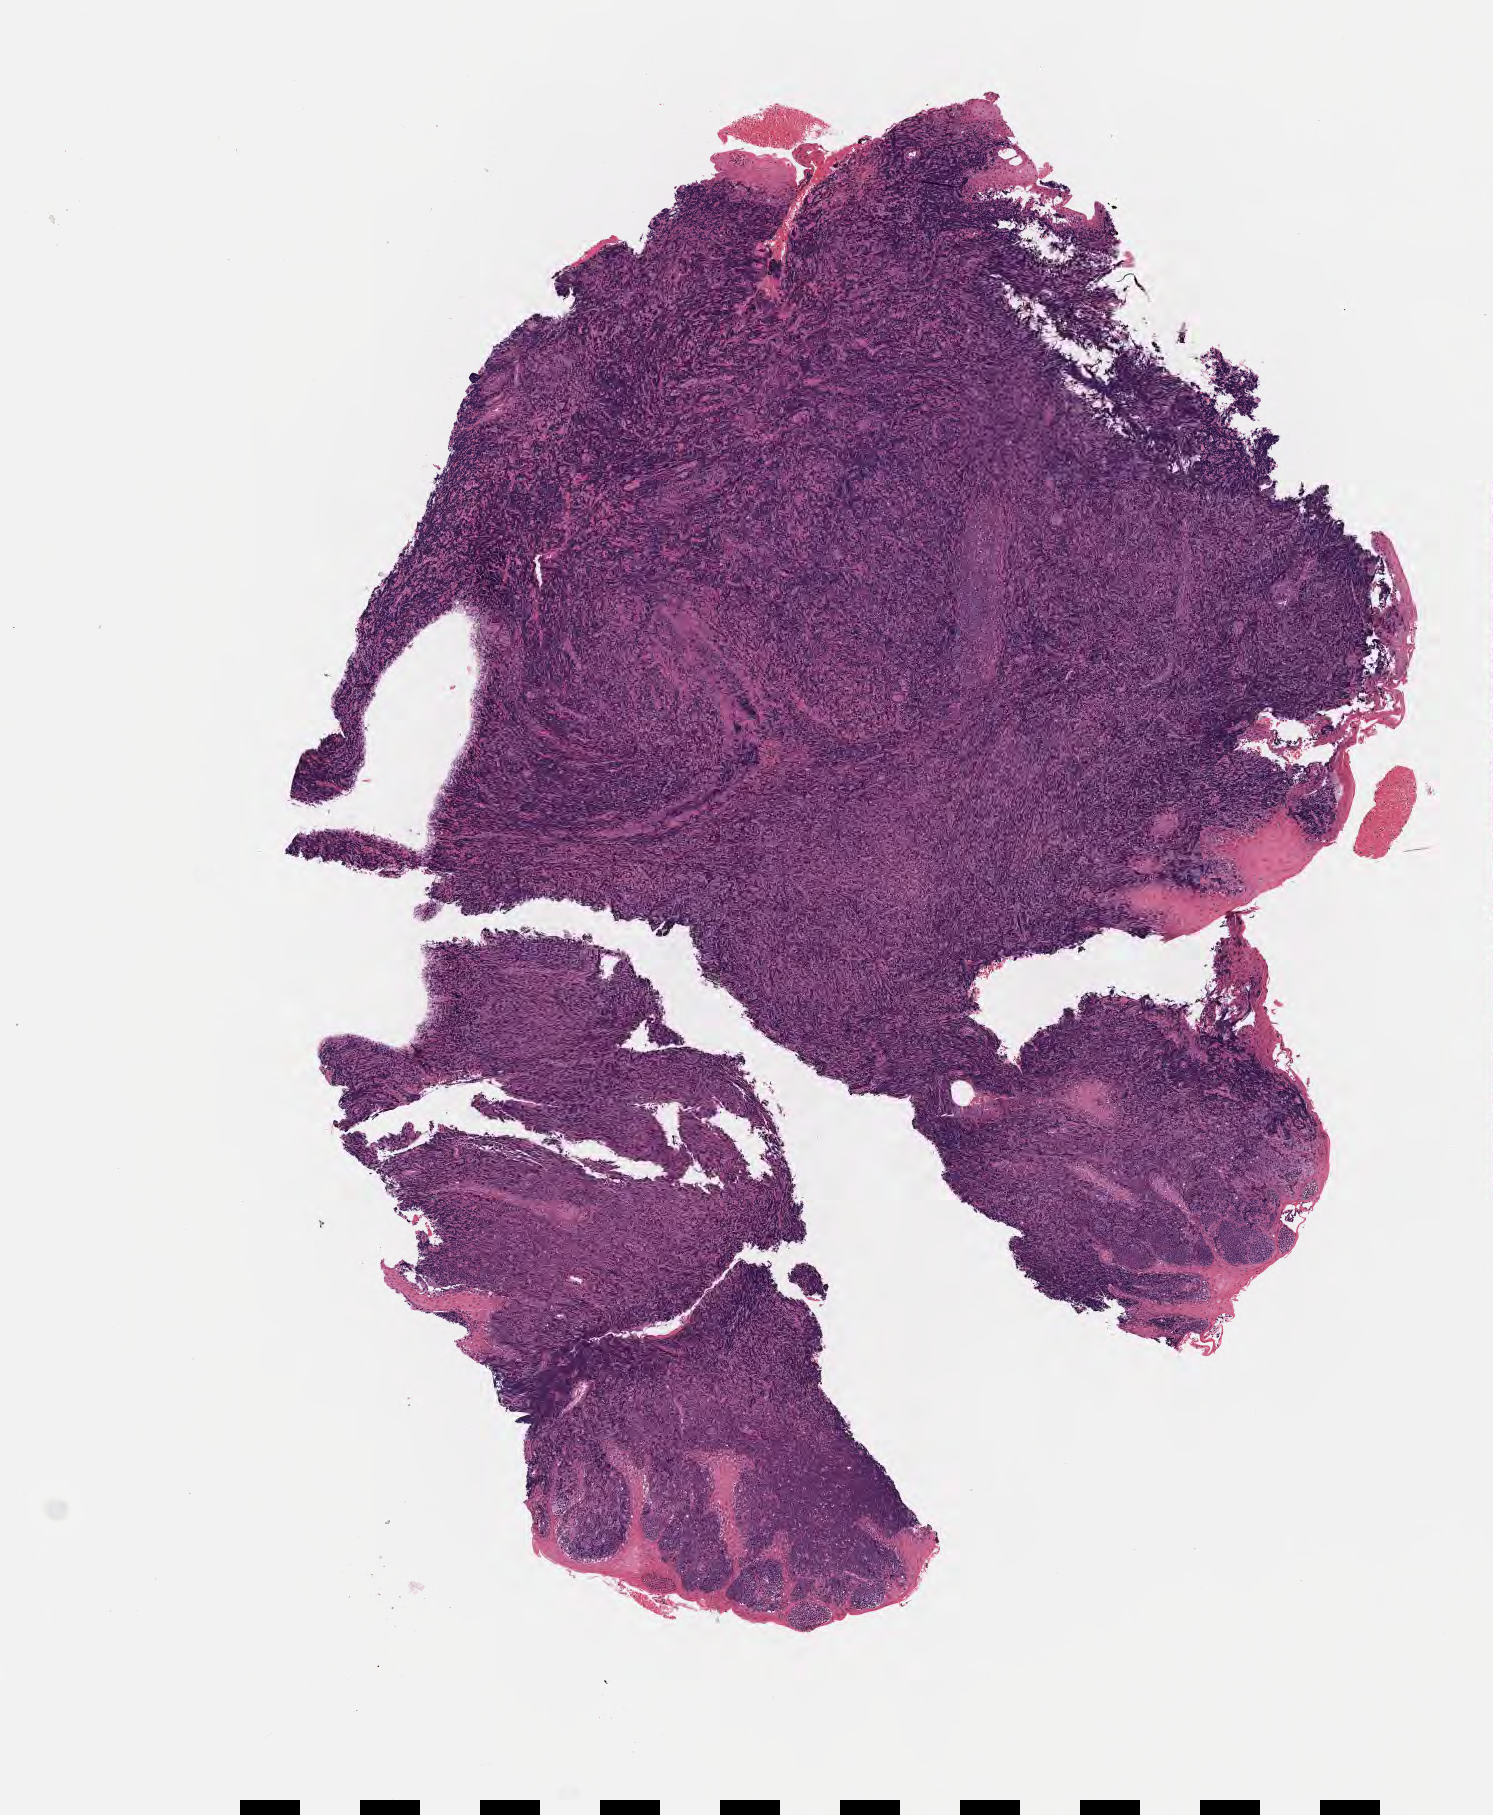
Whole-slide image, hematoxylin and eosin (H&E) stain, low-resolution overview of the scanned area, about 6.0 x 7.3 mm, tumor tissue, site: cranium. Patient: male, 11 years old.
Diagnosis: Diffuse large B-cell lymphoma, NOS.